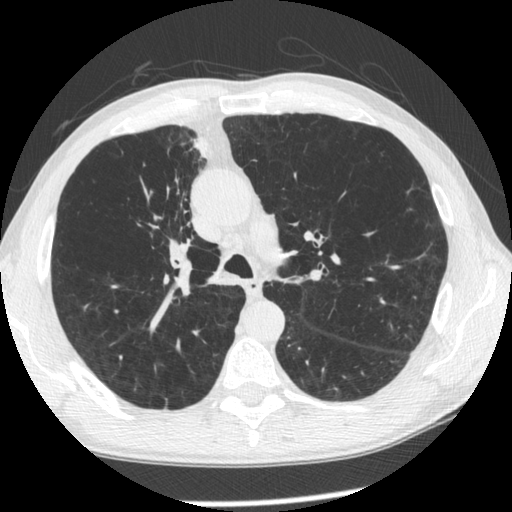
Low-dose screening chest CT, one axial slice; position 158 of 261 along the scan axis; reconstruction kernel STANDARD; lung window (W 1500 / L -600 HU); 512 × 512 image matrix.
Annotated regions visible in this slice (outlined manually by an expert reader):
- lesion 1 (tumor, upper lobe of right lung): box from (x=195, y=135) to (x=209, y=158) px